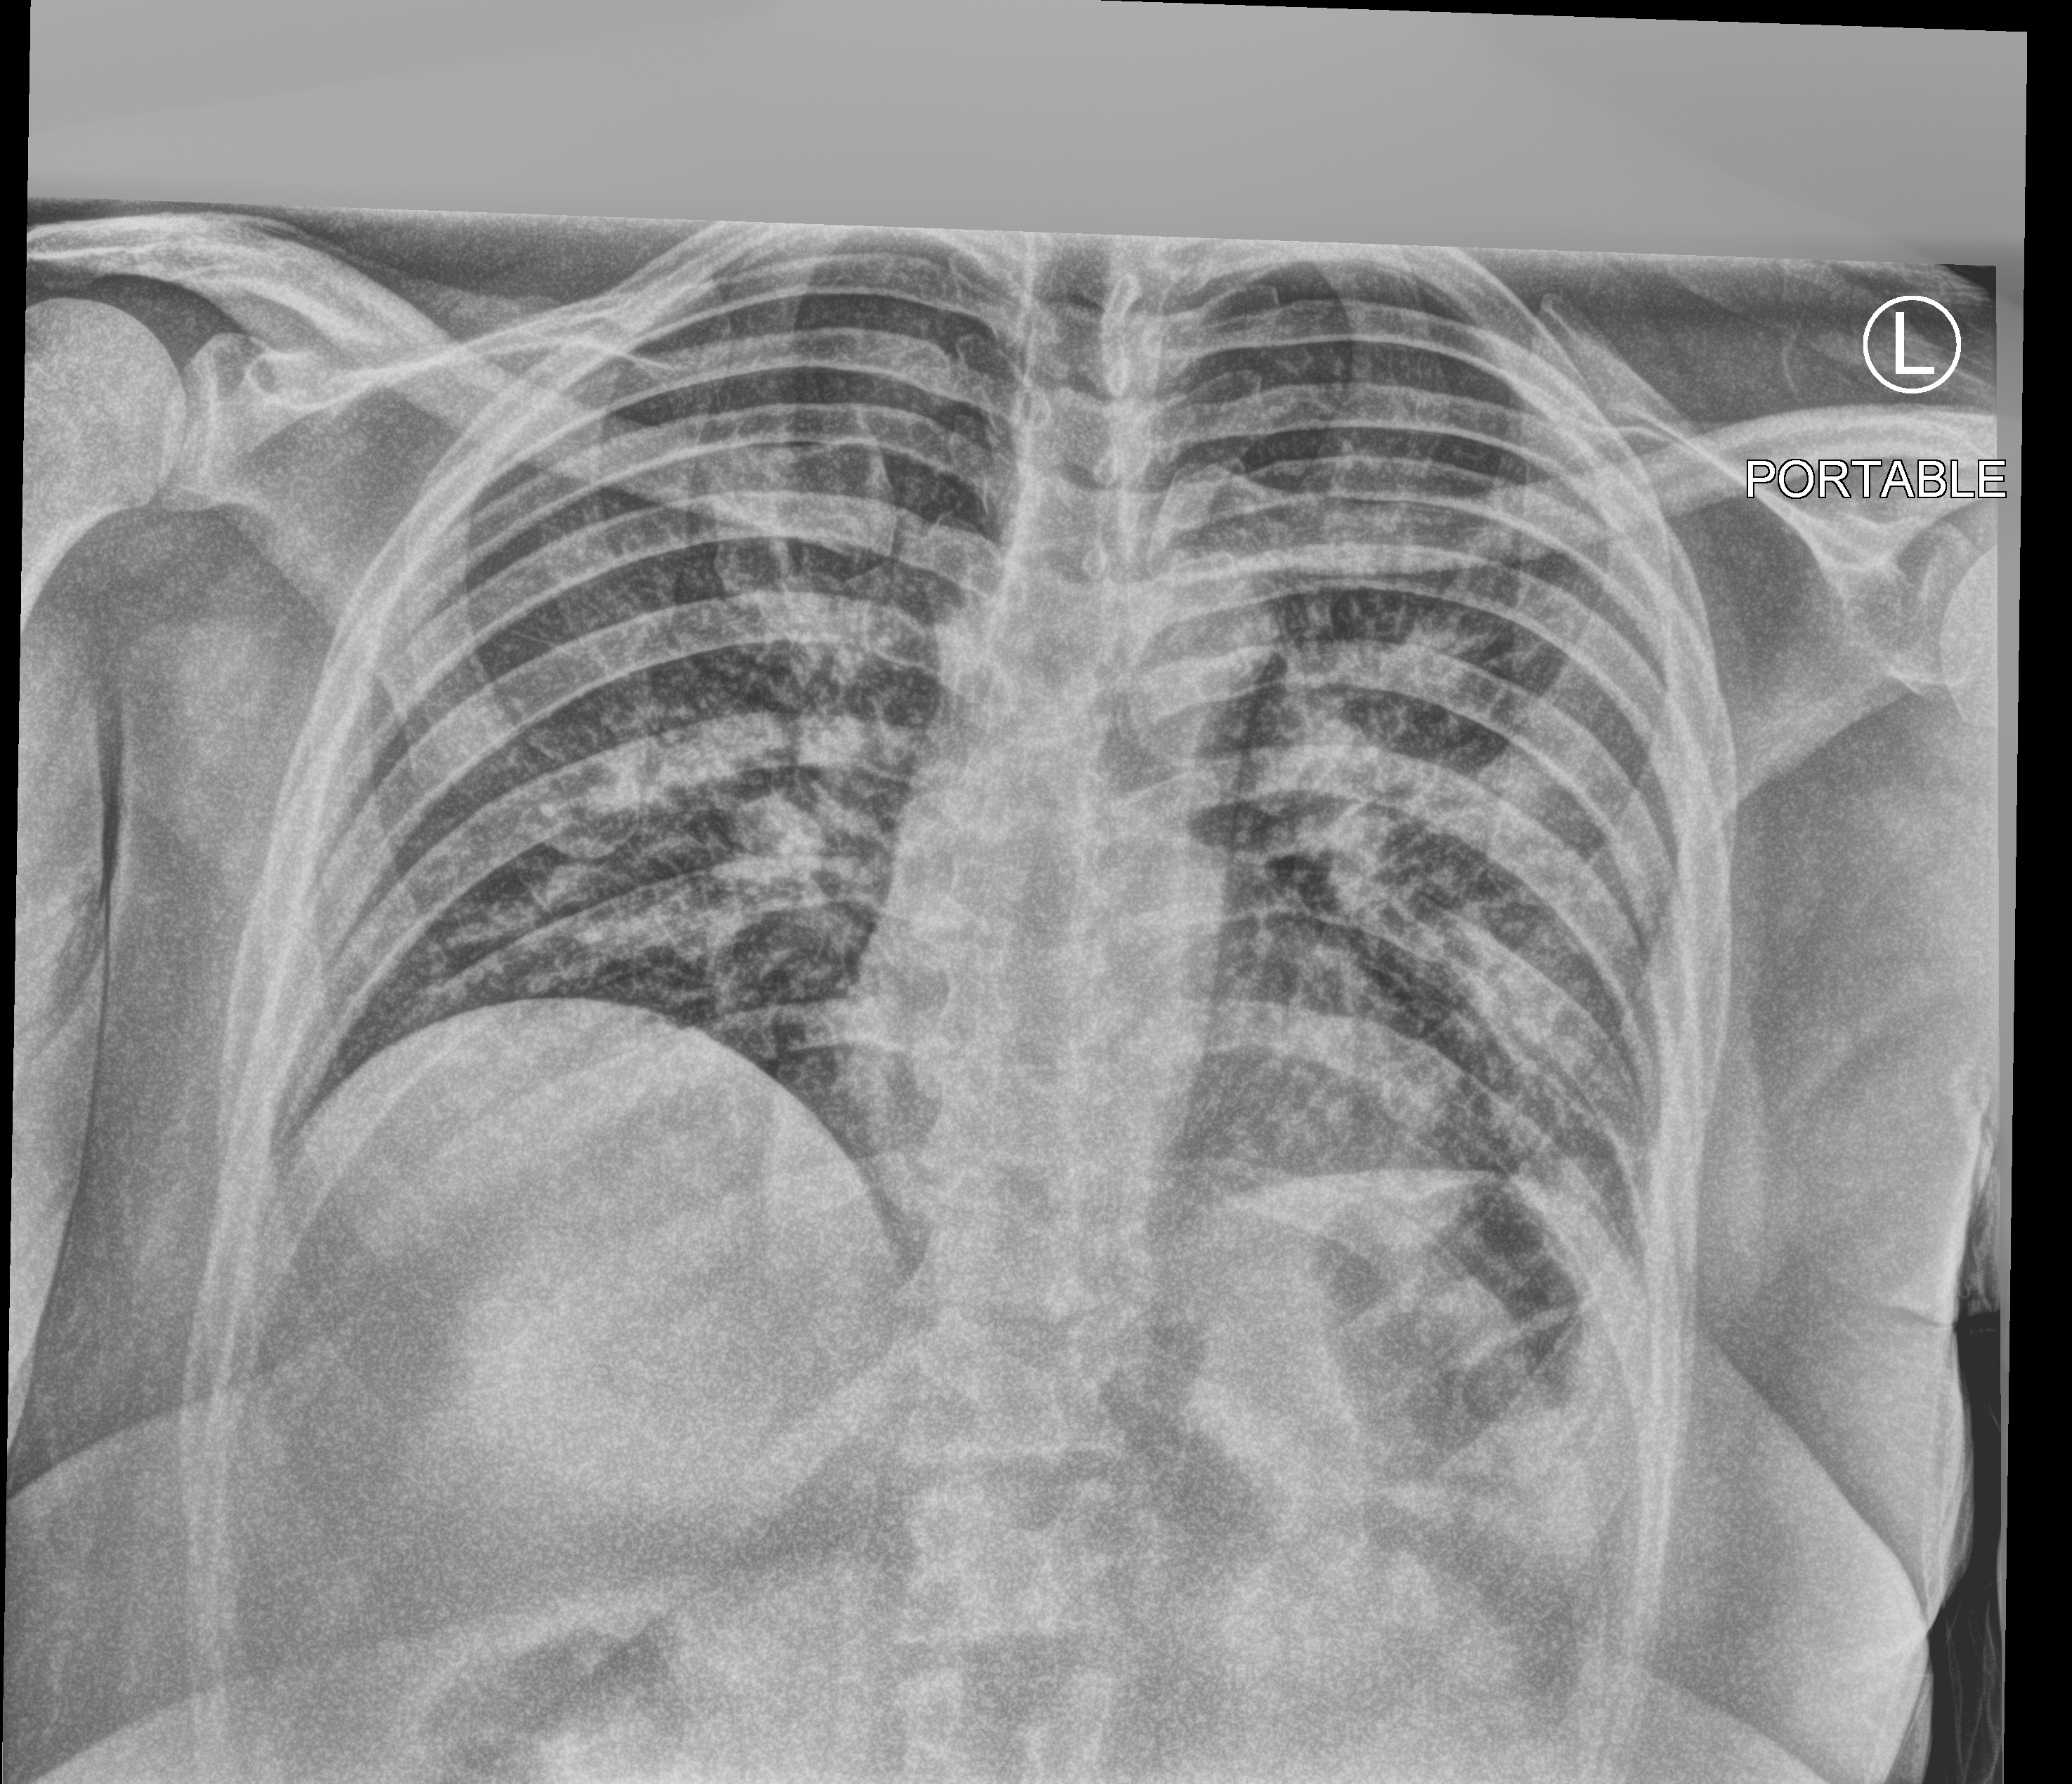
Portable chest radiograph, anteroposterior (AP) projection. Female patient hospitalised with COVID-19, age 18–59 years.
From the hospital-stay record, not from the radiograph (when in the stay this image was taken is not recorded):
- smoking status (admission record): never